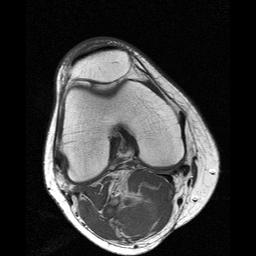
MRI of an extremity soft-tissue mass, one axial slice. Position 7 of 25 along the scan axis. 256 × 256 image matrix, field of view 160 × 160 mm. Female patient. From the clinical record (not read from this slice): histological type: liposarcoma; site of the primary tumour: right thigh.
Outlined on this slice (manually delineated by an expert):
- gross tumour volume (mass): box from (x=98, y=193) to (x=158, y=239) px